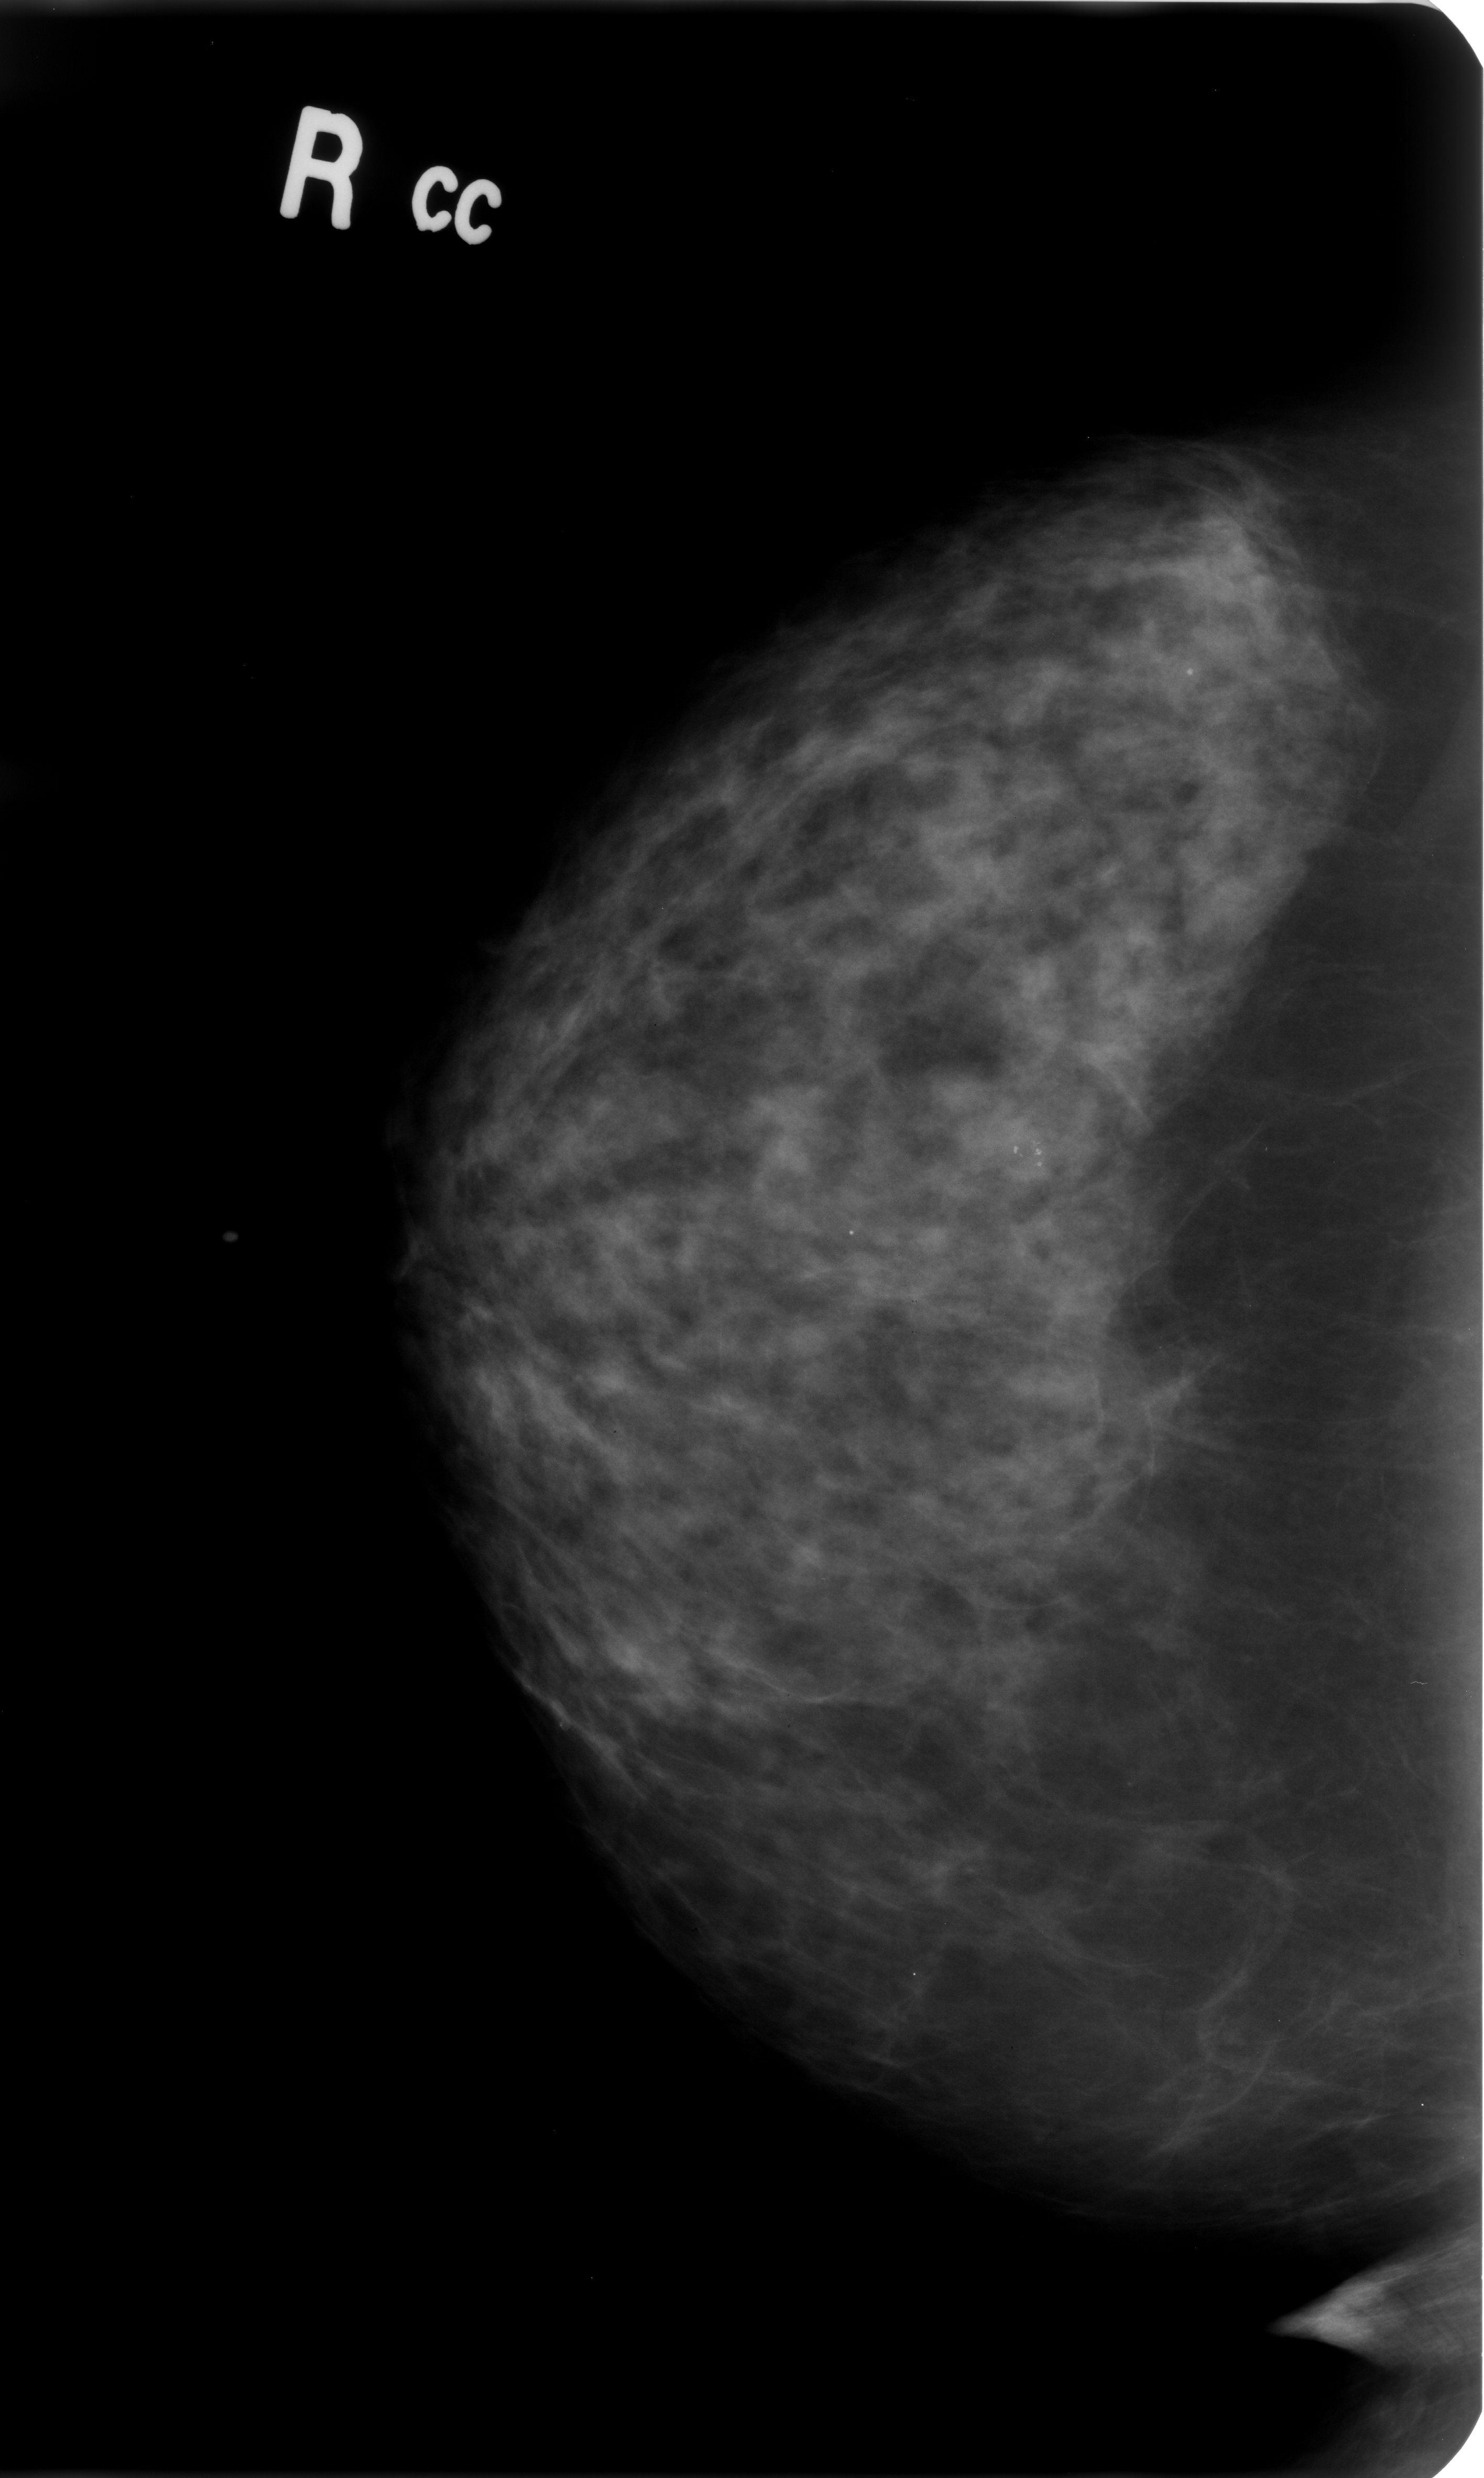
Digitized screen-film mammogram; right breast; CC view; breast composition: heterogeneously dense (BI-RADS density category 3 of 4).
- Marked abnormality: calcifications, morphology pleomorphic, distribution clustered; BI-RADS assessment category 4; pathology (as recorded): benign.